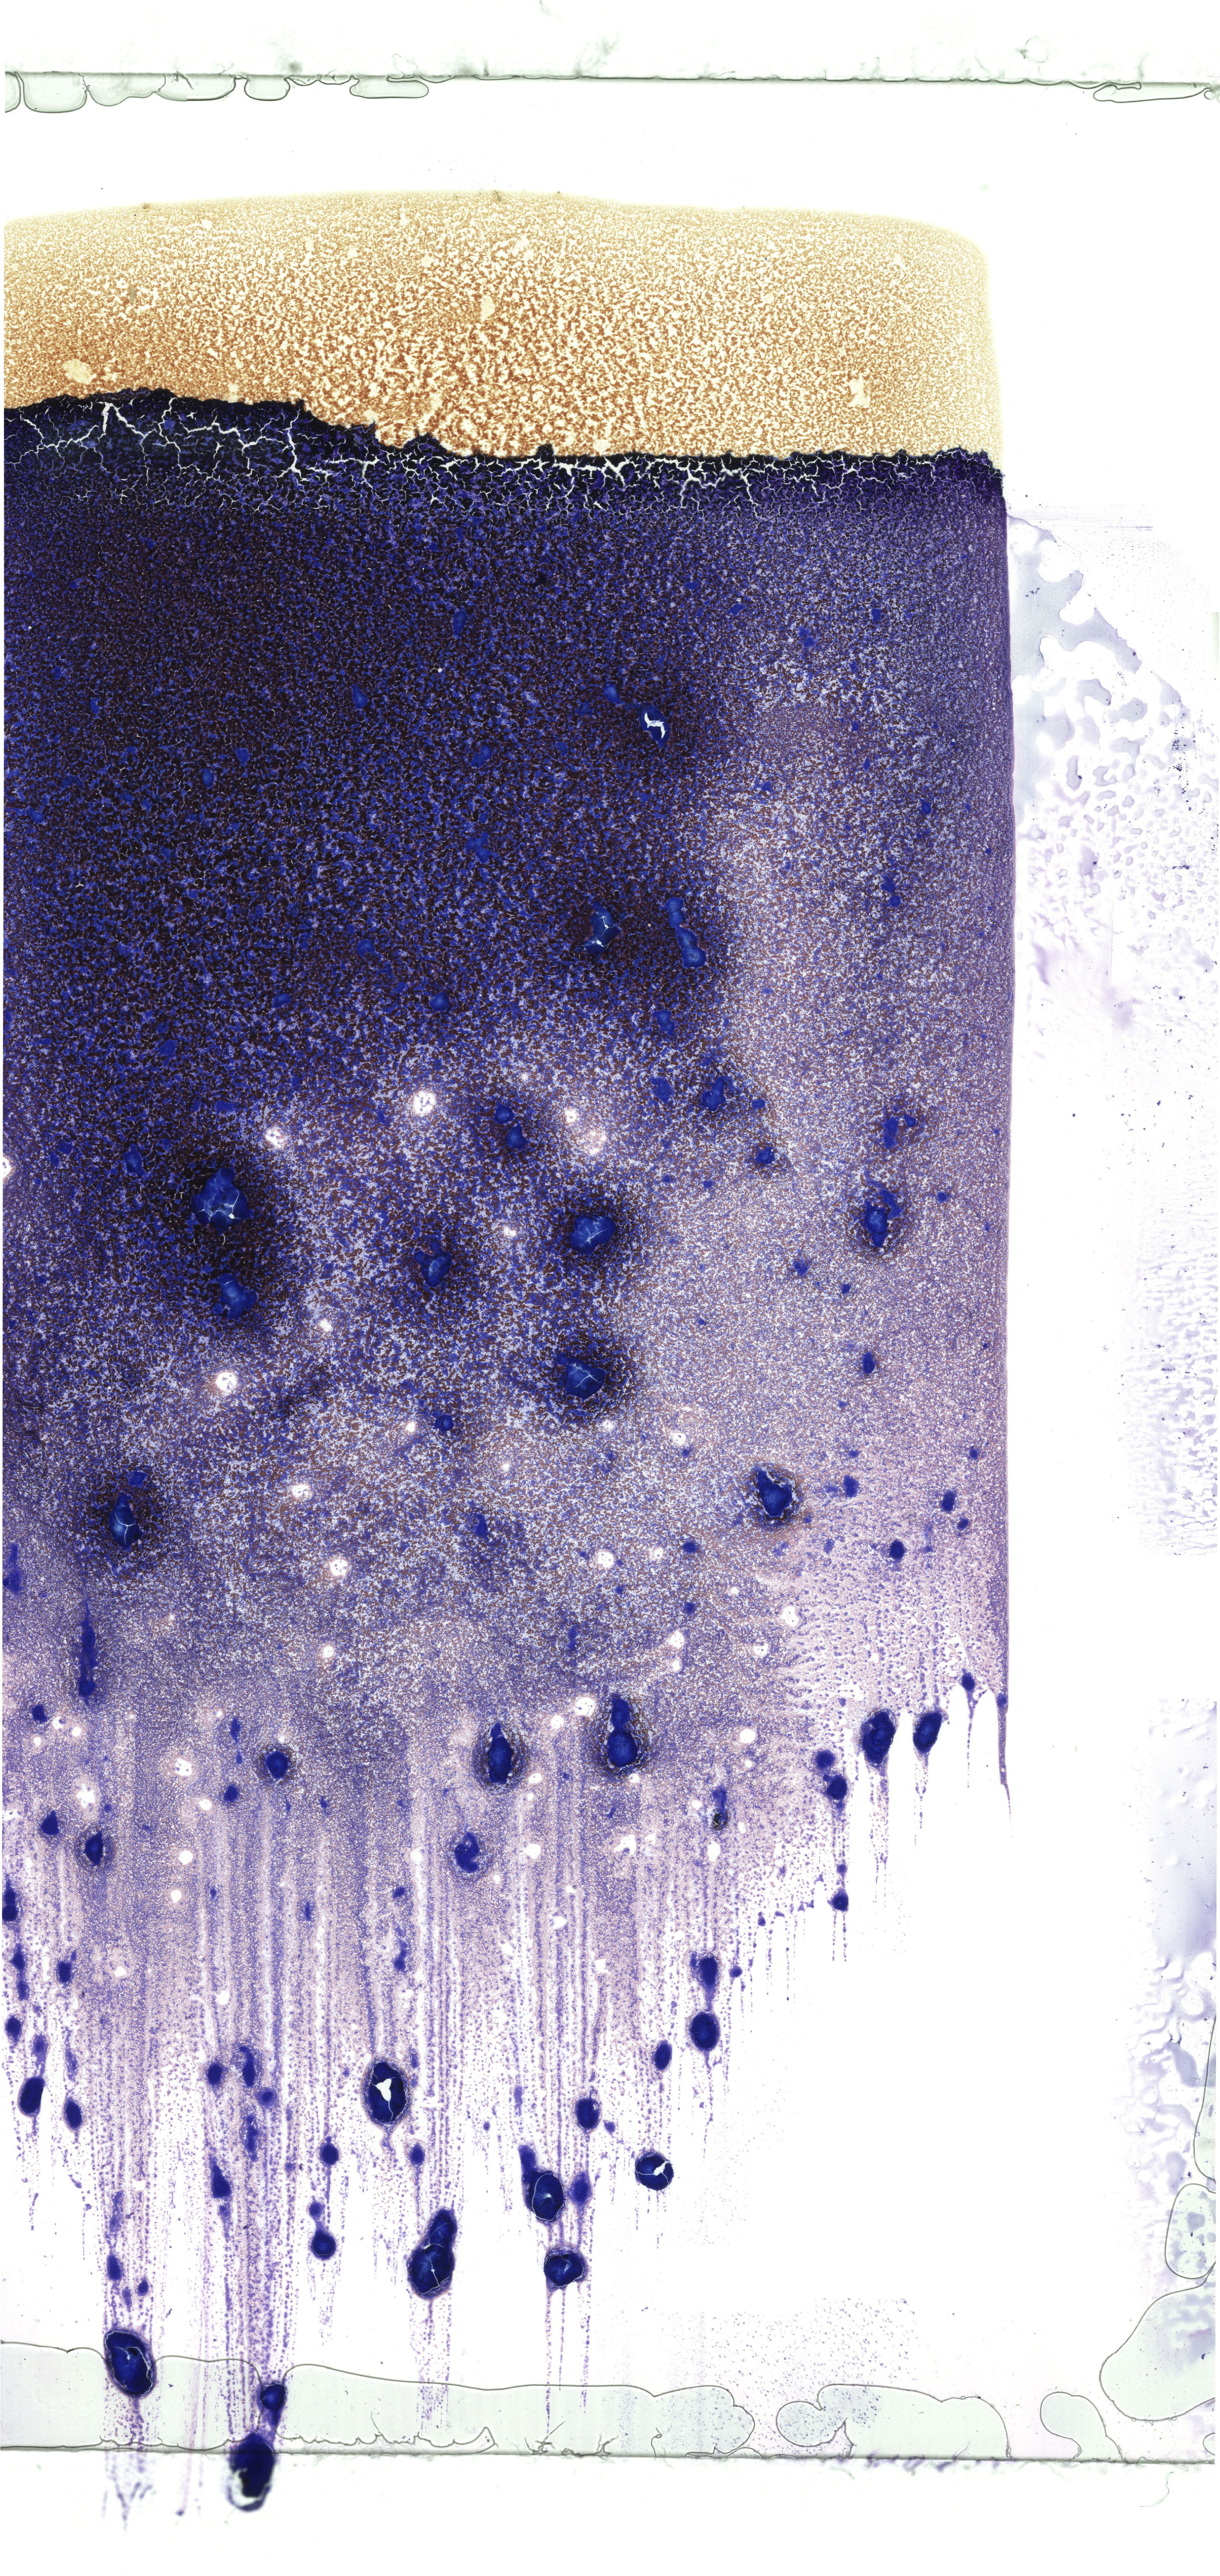
Bone marrow aspirate smear, May-Grünwald–Giemsa stain, whole-slide image — low-resolution overview of the scanned area, about 20.6 x 43.5 mm. Female patient.
Diagnosis: Acute Myeloid Leukemia without Maturation.